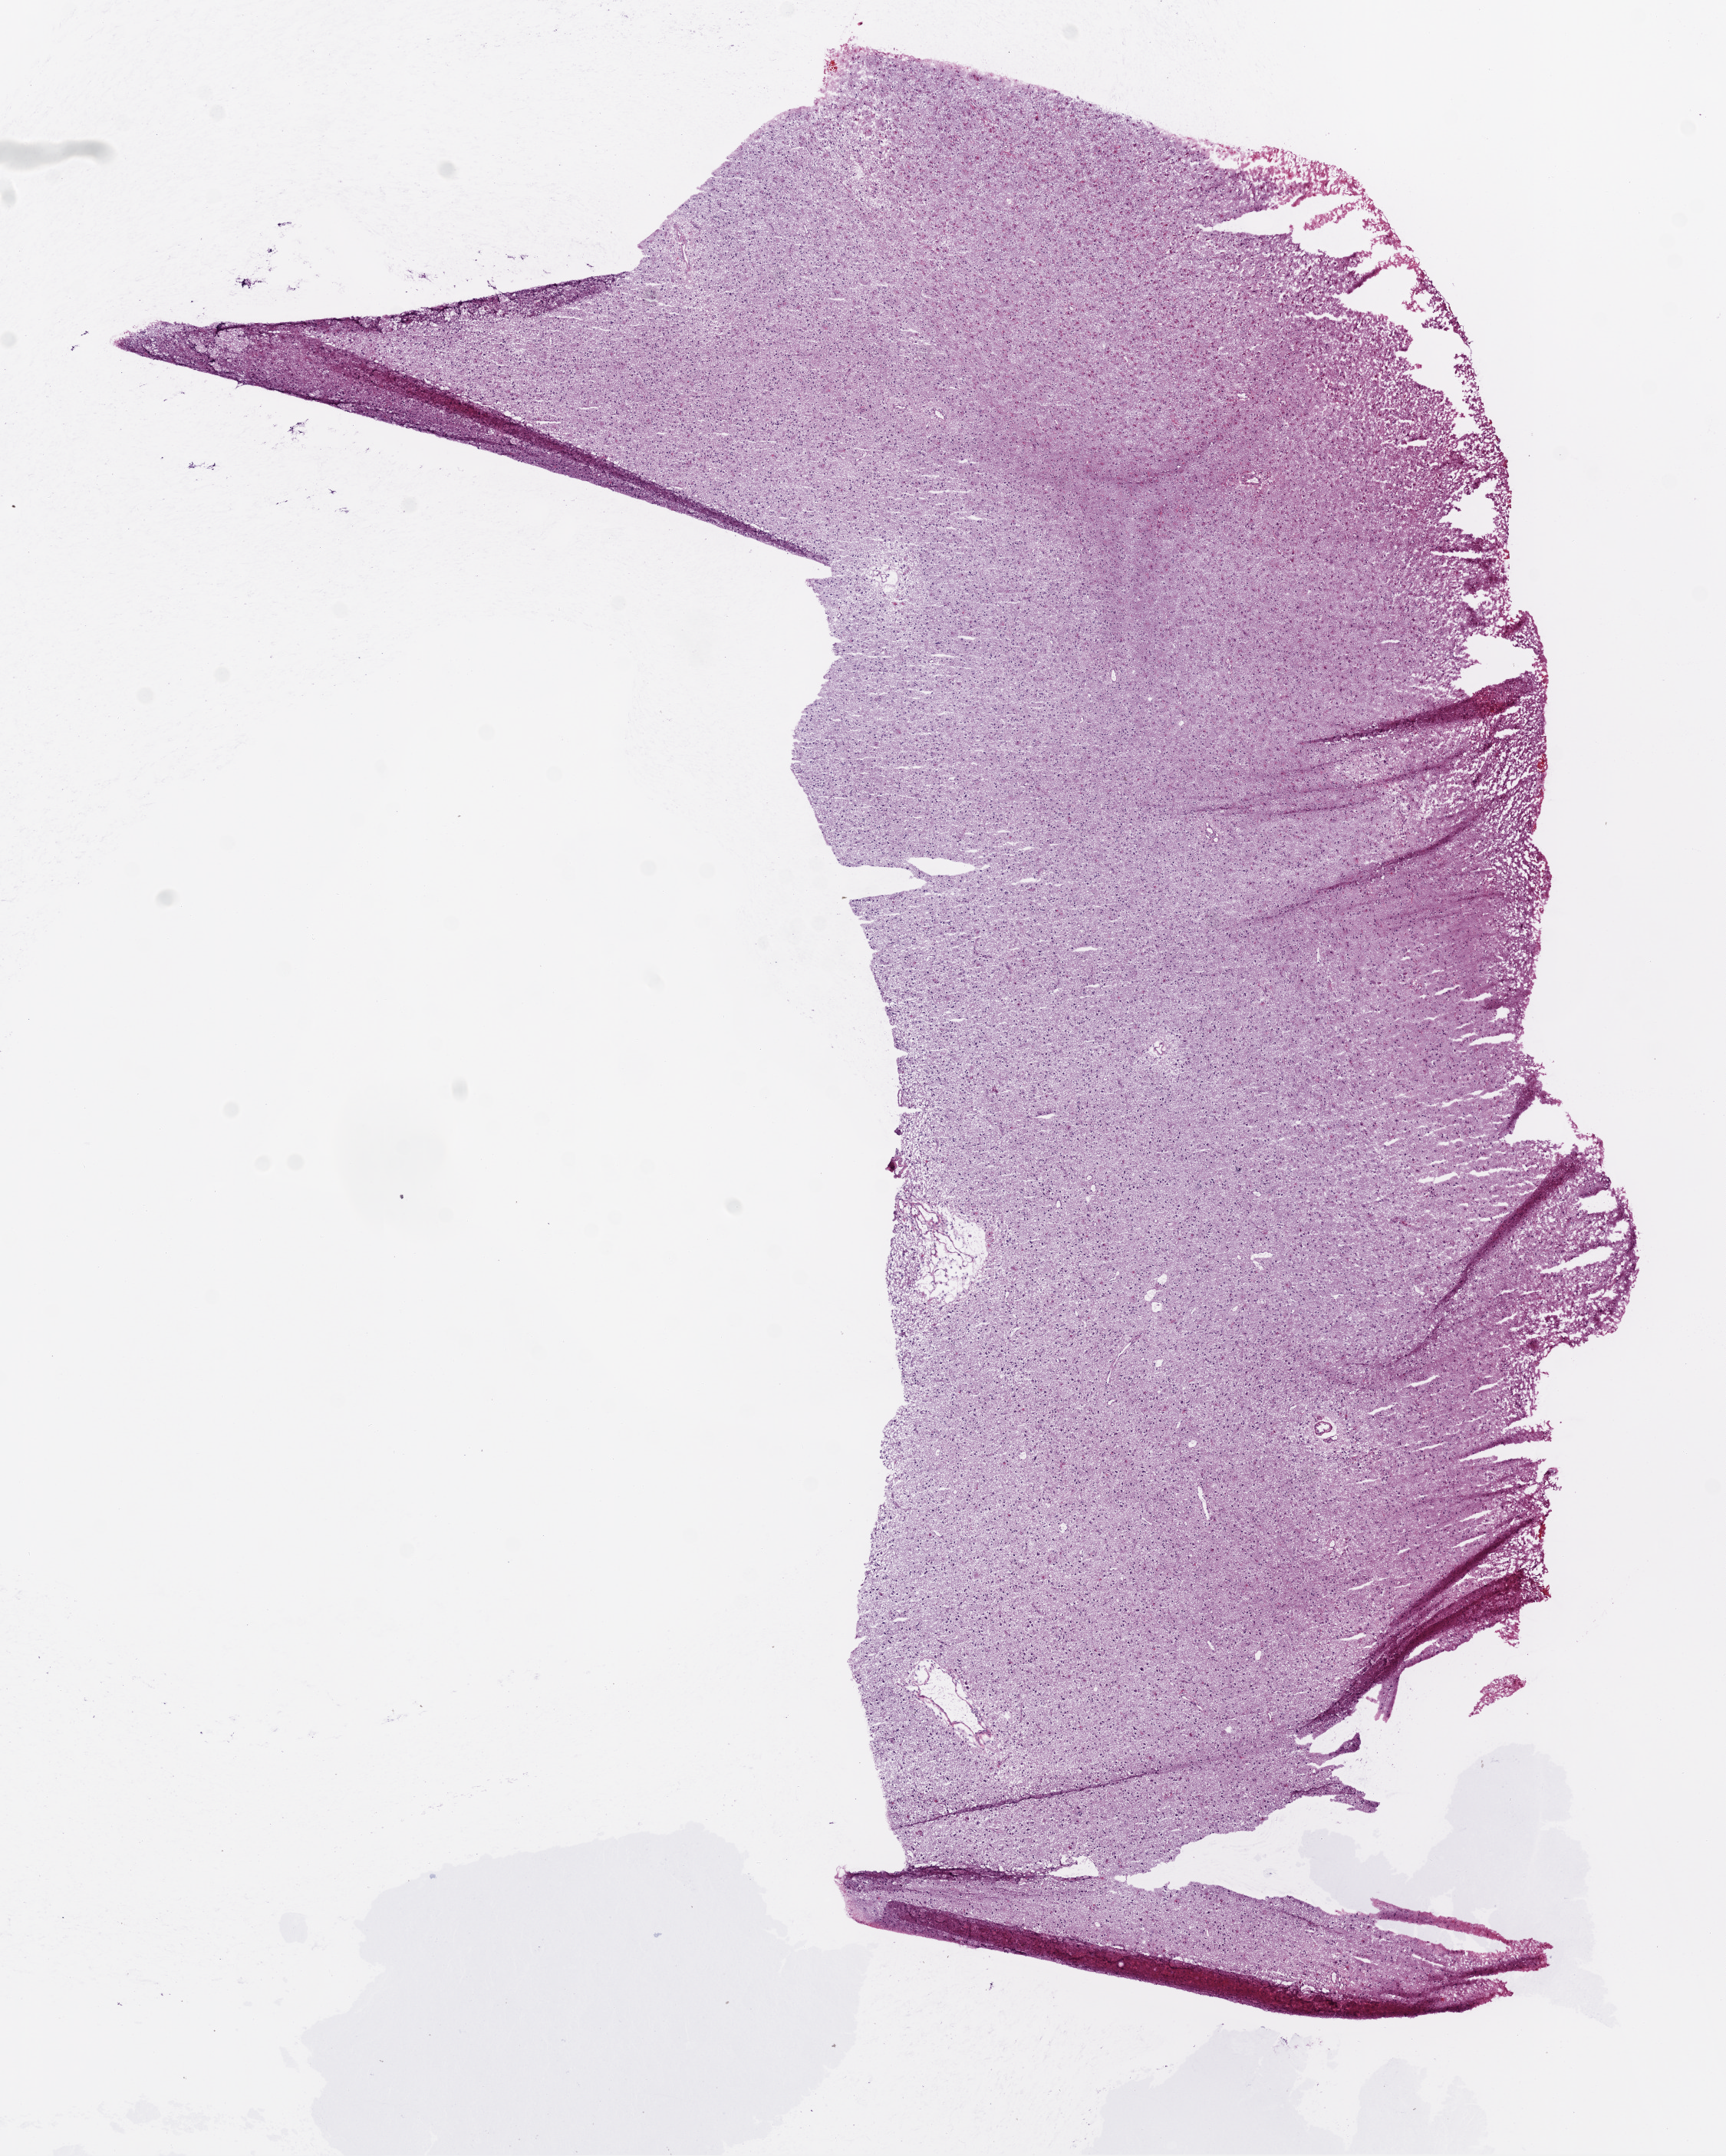
Digitized H&E tissue section (whole slide) — shown as a low-resolution overview of the whole scanned area (about 9.0 x 11.3 mm, acquisition: 20x scan). Frozen section. Brain, primary tumour sample. Female, age 63 years at initial diagnosis. Pathologist review of this section (percent, as recorded): tumour cells 100%, tumour nuclei 80%, normal cells 0%, stromal cells 0%, necrosis 0%.
Diagnosis: Glioblastoma.